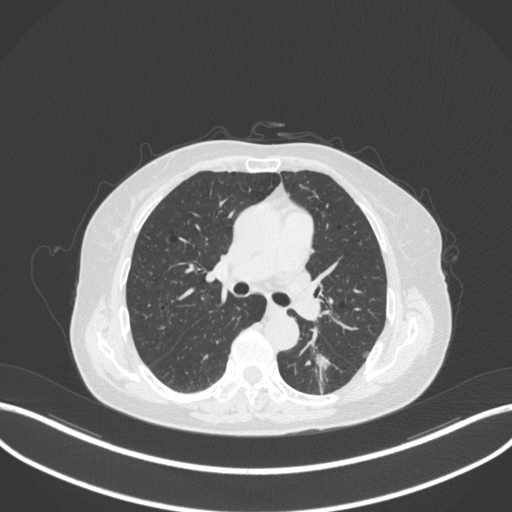
Chest CT, one axial slice; slice 176 of 352 in the series (ordered by position); reconstruction kernel B31f; lung window (W 1500 / L -600 HU); 1 mm slice thickness; 512 × 512 image matrix, field of view 400 × 400 mm. Patient: female, 70 years. From the clinical record (not read from this slice): clinical TNM (as recorded): T1c N0 M0.
Annotated regions visible in this slice (rectangle marked by the reading radiologist):
- lung tumour (recorded histology: adenocarcinoma): box from (x=301, y=339) to (x=342, y=391) px